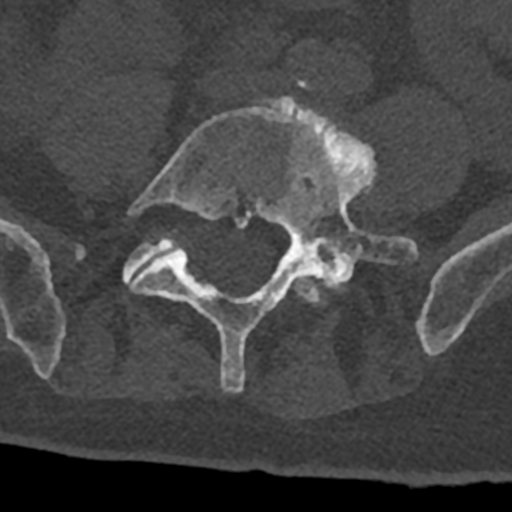
CT including the spine, one axial slice; slice 203 of 797 in the series (ordered by position); bone window (W 1800 / L 400 HU); 512 × 512 image matrix. Patient: male, 74 years. From the clinical record (not read from this slice): primary cancer: renal; vertebrae with lytic lesions (as recorded): T10, L1, L2, L3, L4, L5.
Outlined on this slice (semi-automatically segmented with operator editing):
- L4 vertebra: bounding box <289,276,323,304> (left, top, right, bottom; pixels)
- L5 vertebra: <128,97,418,393>